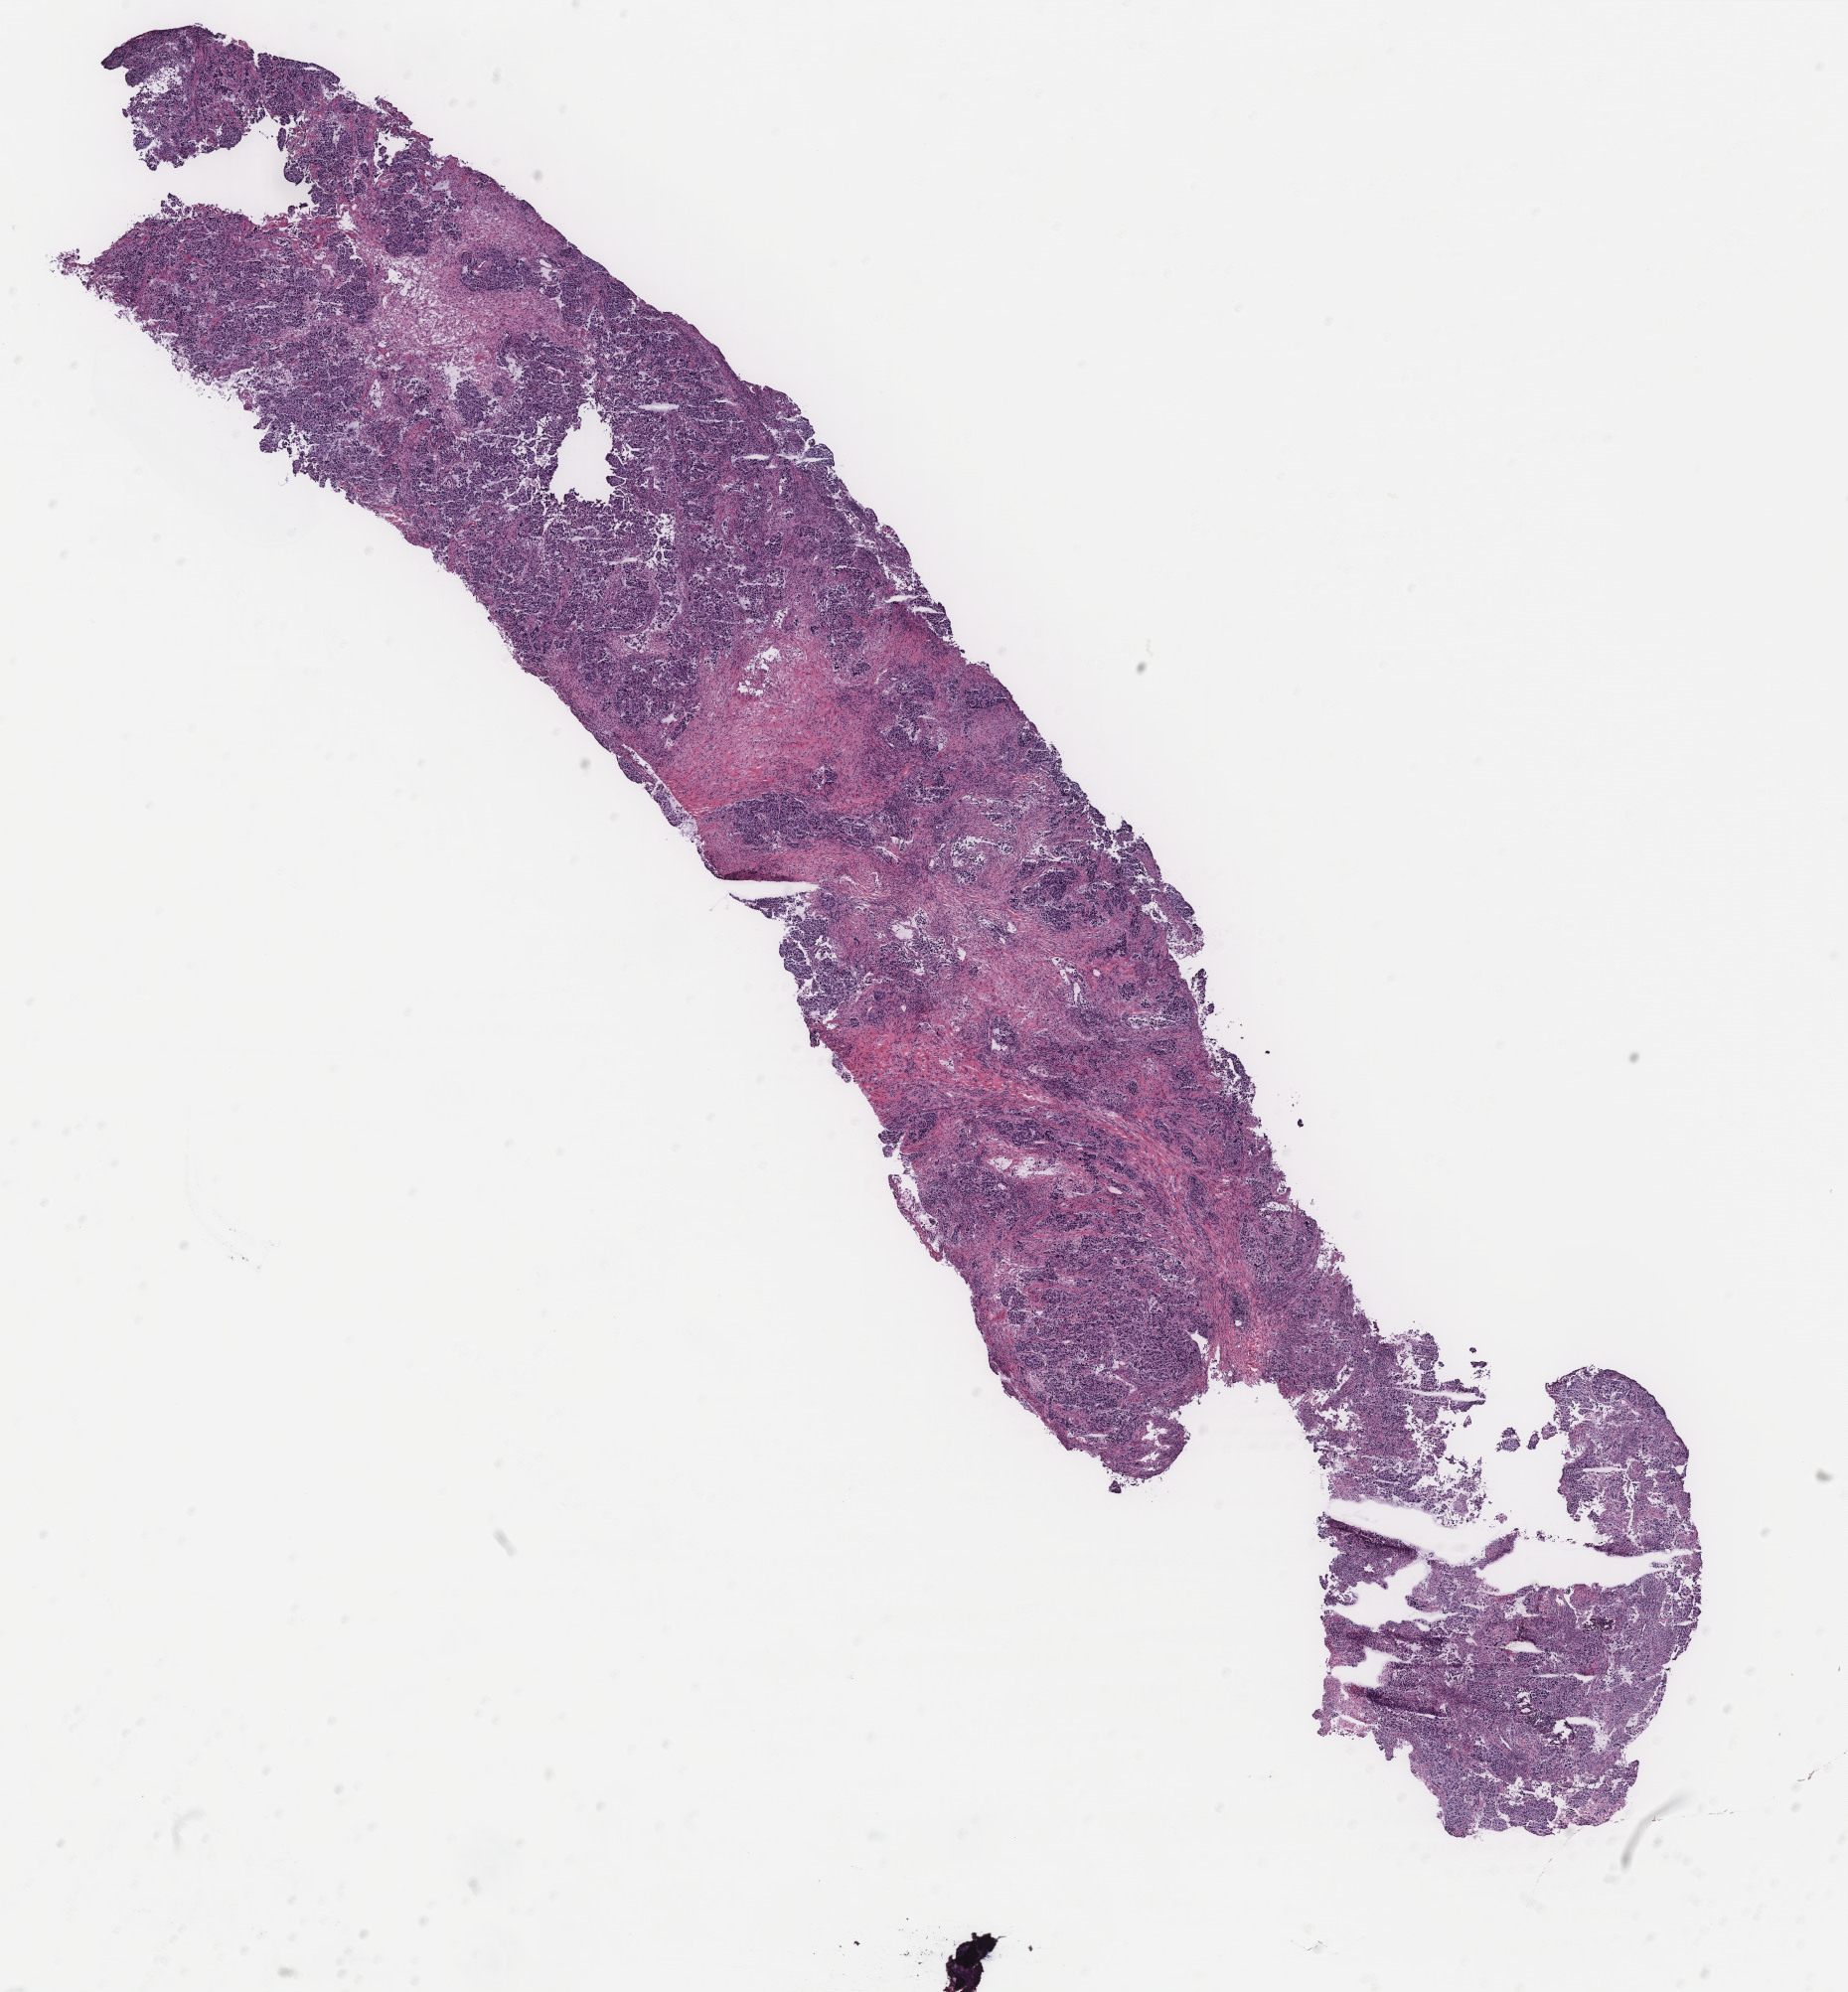
Hematoxylin and eosin (H&E) stained whole-slide image — shown as a low-resolution overview of the whole scanned area (about 14.9 x 16.0 mm); breast, tumour tissue. 80-year-old female patient.
AJCC pathologic stage: IIA. Diagnosis: Infiltrating duct carcinoma, NOS.